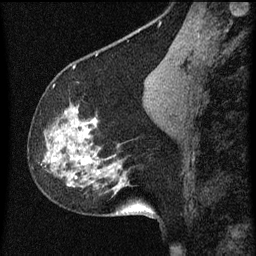
Breast MRI (dynamic contrast-enhanced), one sagittal slice; slice 27 of 60 in the series (ordered by position); dynamic contrast-enhanced series, image 2 of 3 at this slice position (ordered by acquisition); 1.5 T; TE 4.2 ms, TR 8 ms; 2 mm slice thickness; 256 × 256 image matrix, field of view 180 × 180 mm. Patient: female, 61 years.
Outlined on this slice (semi-automatic segmentation, software-assisted and operator-edited):
- analysis volume of interest (the breast-tissue region the enhancement analysis was run in; not a lesion): box from (x=32, y=80) to (x=139, y=209) px
- tumour enhancement mask (voxels above the 70 % enhancement threshold inside the analysis volume of interest): (x=53, y=118)–(x=95, y=179)